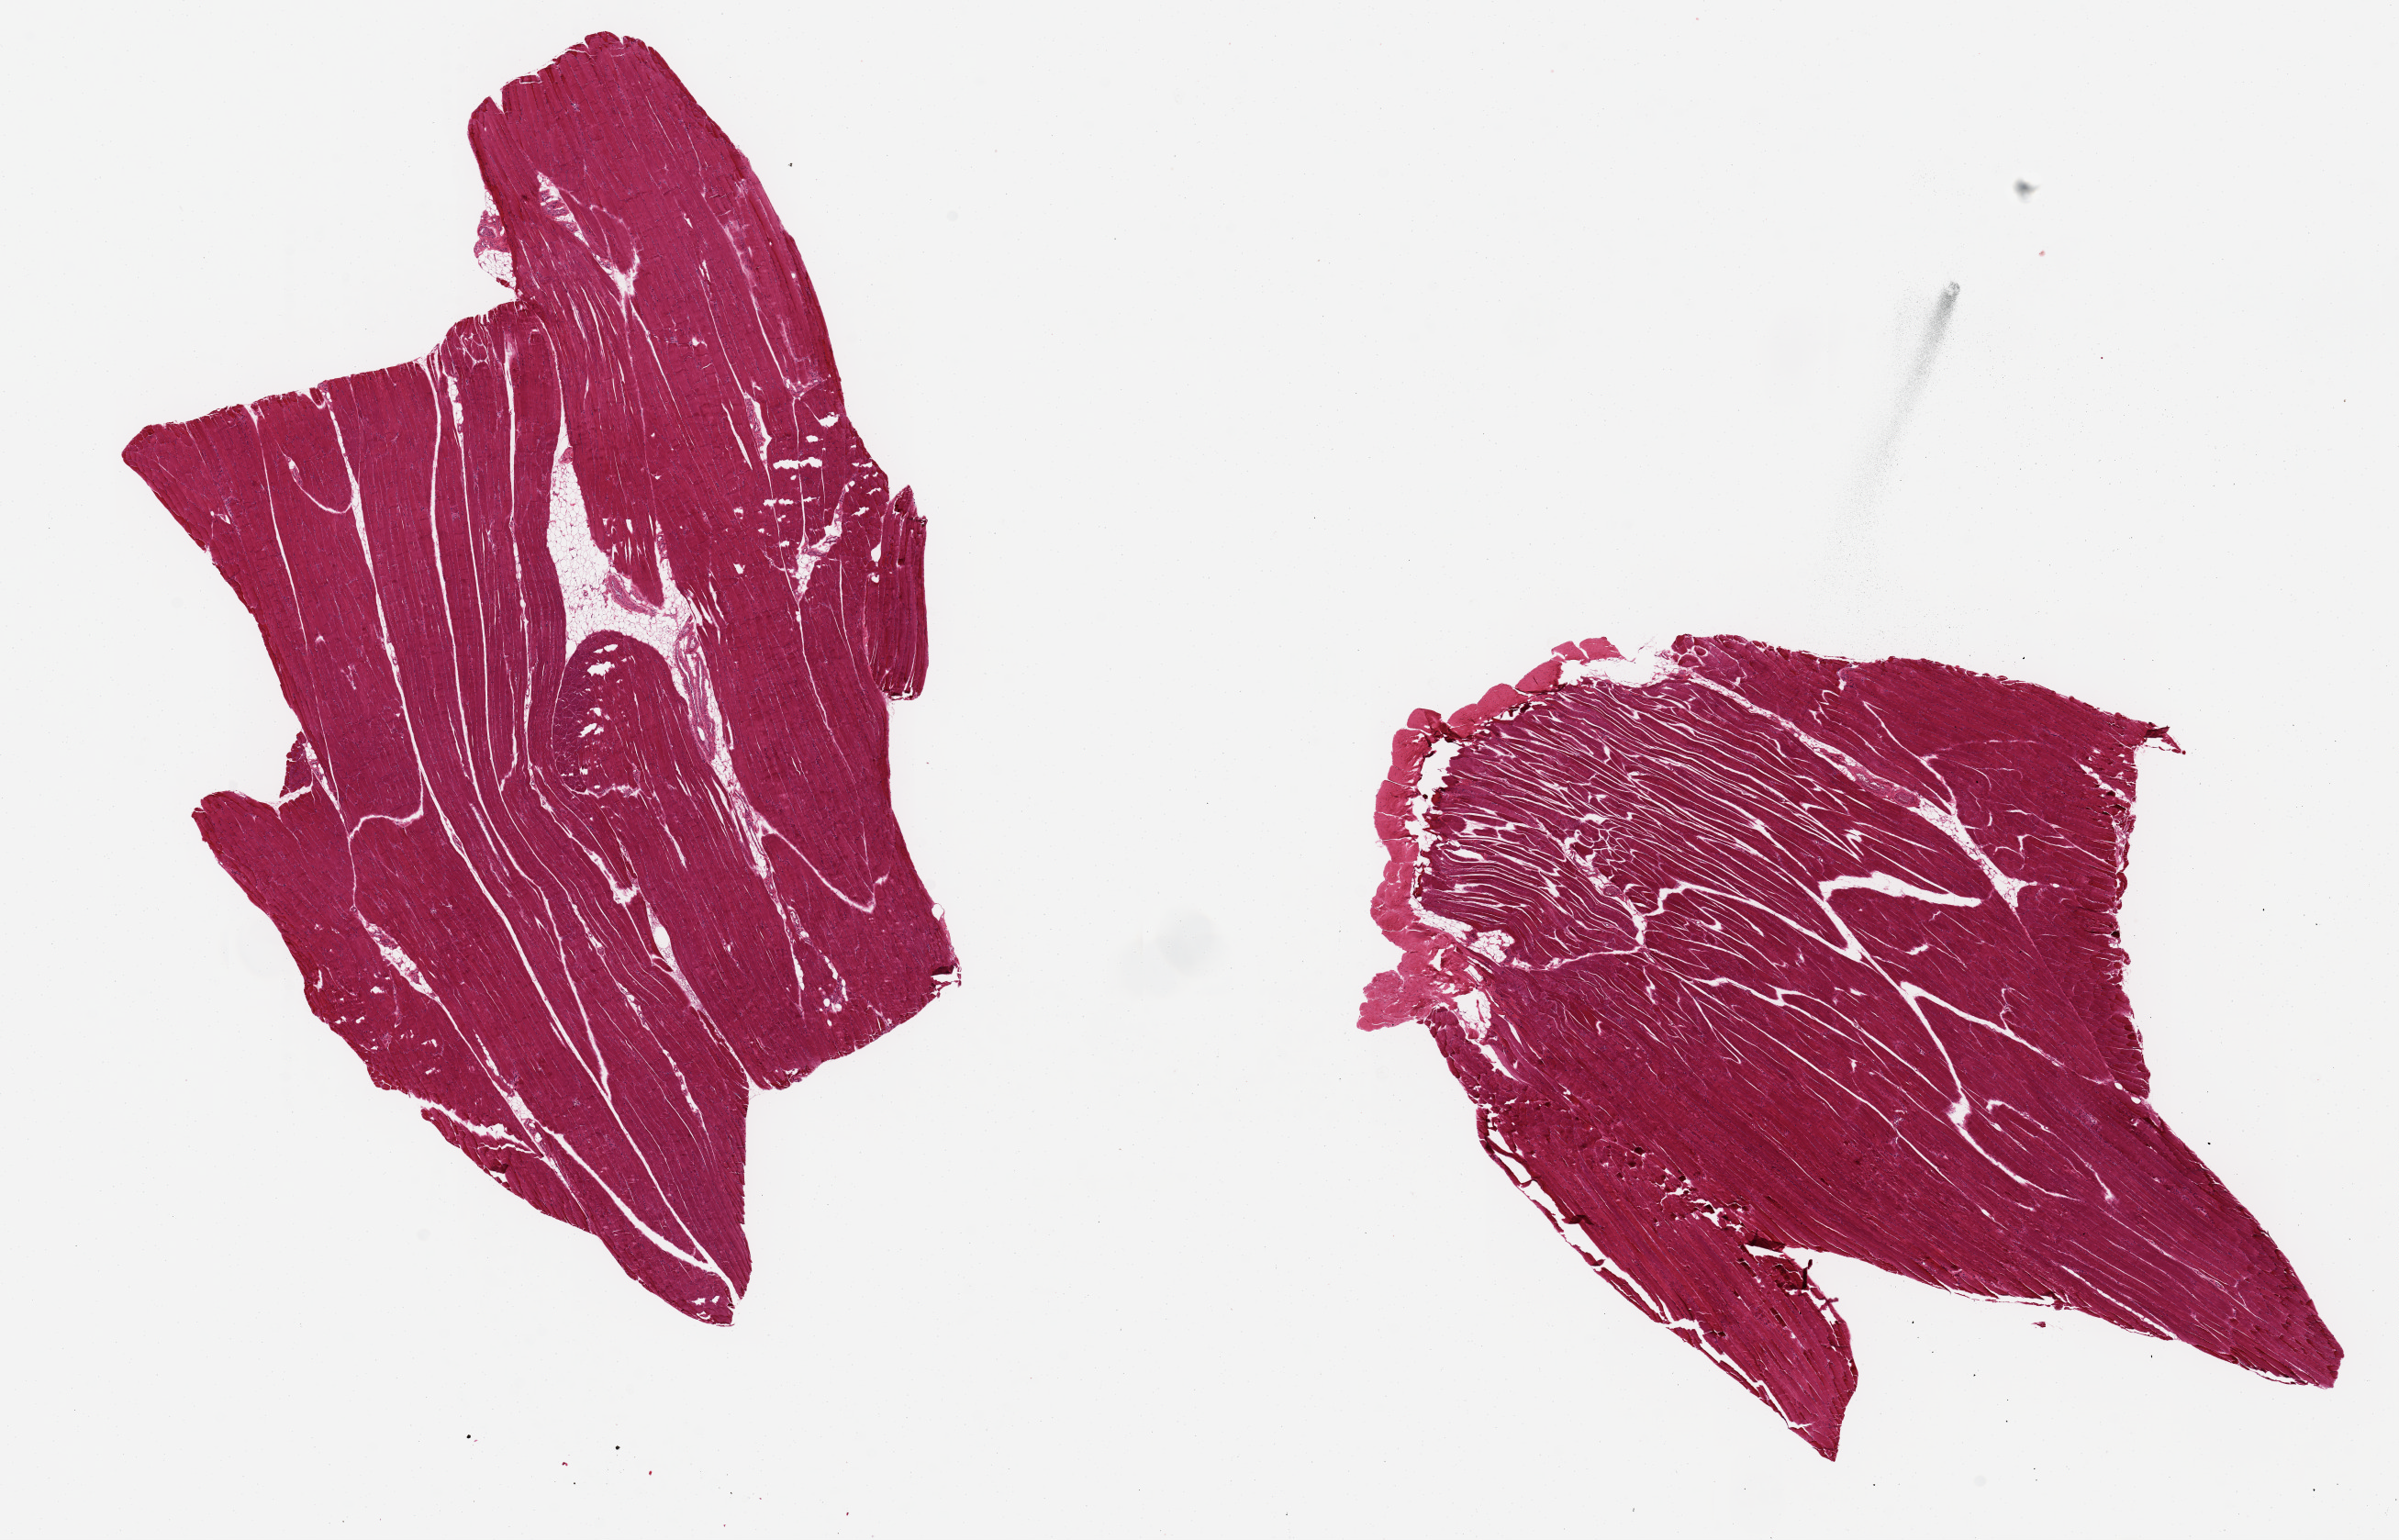
Whole-slide image, haematoxylin and eosin stain, brightfield — shown as a low-resolution overview of the whole scanned area (about 20.7 x 13.3 mm, acquisition: 20x scan); PAXgene-fixed paraffin-embedded (PFPE) section; target tissue: skeletal muscle; tissue donor sample.
- review note (as recorded): 2 pieces, 9x6 & 9x7 mm; minimal adipose